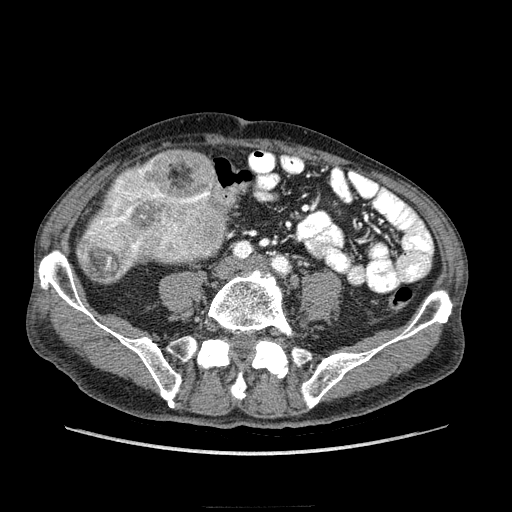
Contrast-enhanced abdominal CT (liver protocol), one axial slice. 100 kVp. Soft-tissue window (W 400 / L 40 HU). 2.5 mm slice thickness. 512 × 512 image matrix, field of view 380 × 380 mm. Case-level facts recorded for this patient, not image findings: diagnosis: hepatocellular carcinoma (patient treated with transarterial chemoembolisation; whether this scan precedes or follows treatment is not stated here); TNM stage (as recorded): Stage-IIIA; Child-Pugh class: A; tumour nodularity: multinodular.
Outlined on this slice (semi-automatically segmented with operator editing):
- mass: bounding box <75,149,236,284> (left, top, right, bottom; pixels)